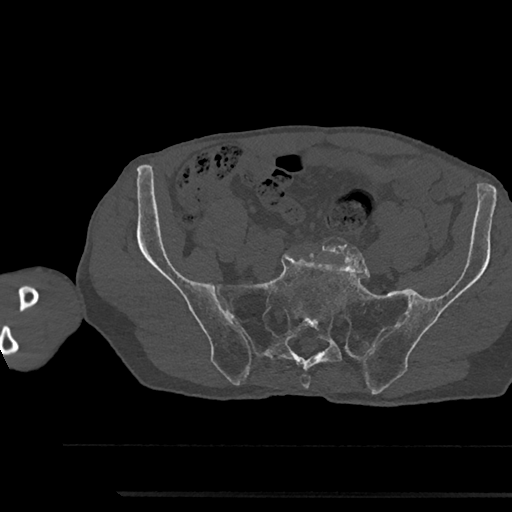
CT including the spine, one axial slice. Slice 272 of 797 in the series (ordered by position). Reconstruction kernel Br40s/3. Bone window (W 1800 / L 400 HU). 0.5 mm slice thickness. 512 × 512 image matrix, field of view 367 × 367 mm. Male patient, age 79 years. From the clinical record (not read from this slice): primary cancer: prostate.
Annotated regions visible in this slice (semi-automatic segmentation, software-assisted and operator-edited):
- L5 vertebra: bounding box [x1, y1, x2, y2] px = [304, 241, 313, 247]